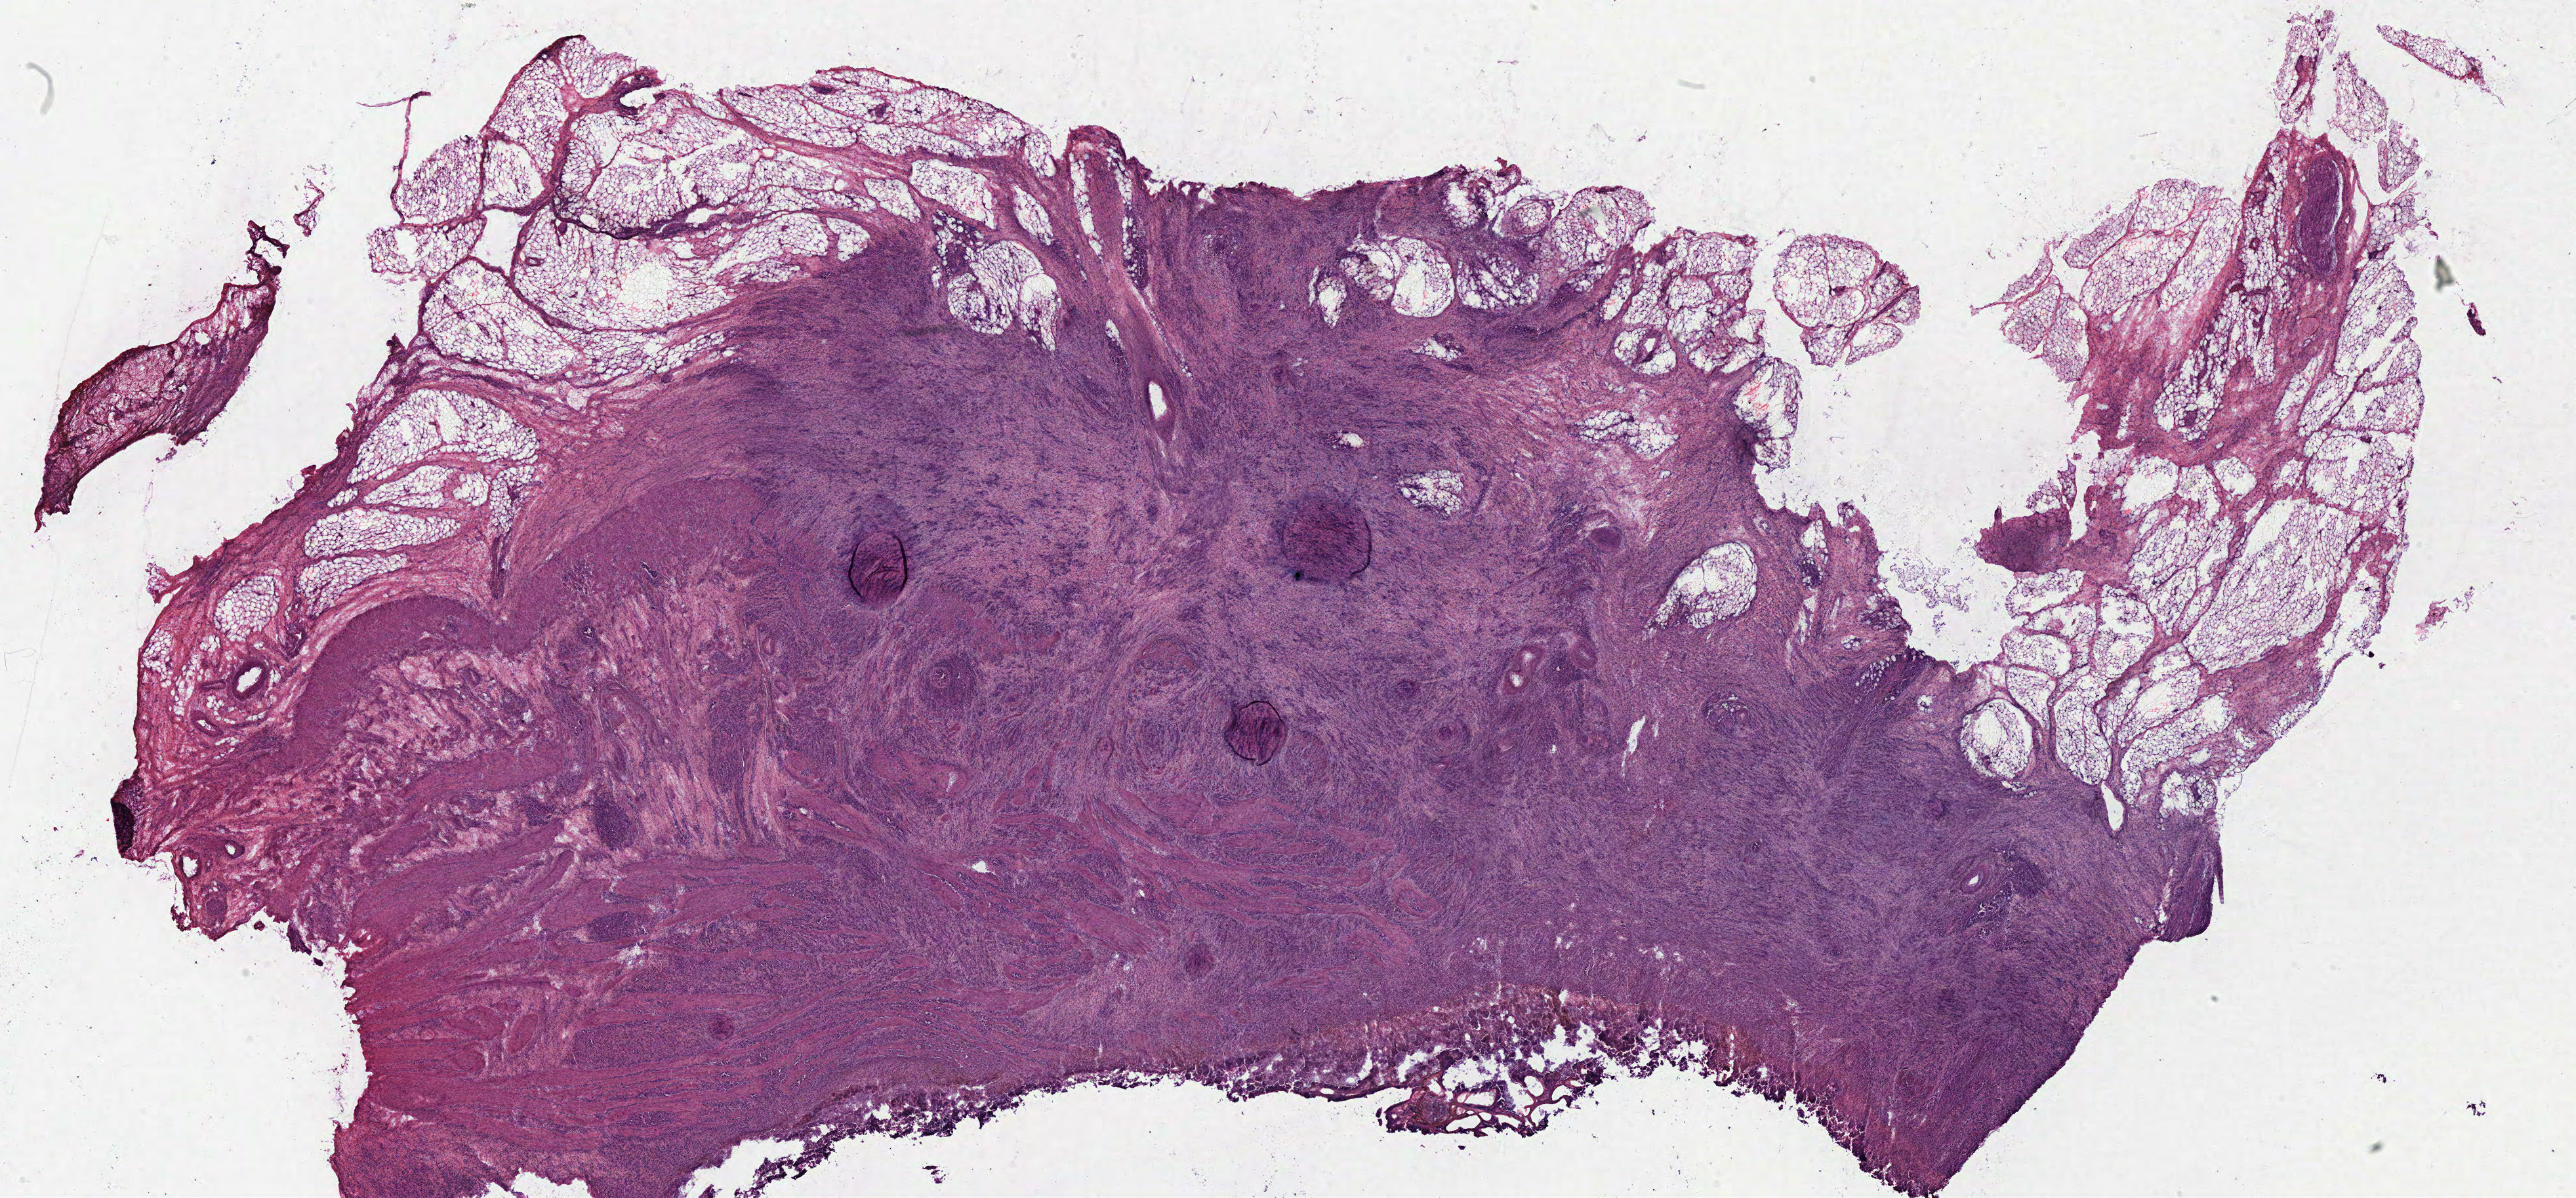
Hematoxylin and eosin (H&E) stained whole-slide image — low-resolution overview of the scanned area, about 30.9 x 14.4 mm (acquisition: 40x scan), frozen section from the bottom of the tissue portion, primary tumour sample from the stomach. Female, age 68 years at initial diagnosis. Histologic grade: G3 (poorly differentiated). Slide review estimates, as recorded: tumour cells 75%, tumour nuclei 75%, normal cells 0%, stromal cells 25%, necrosis 0%.
Lymph nodes positive (case pathology): 9 of 12 examined. AJCC pathologic stage: IIIB (7th edition). Diagnosis: Adenocarcinoma, NOS.